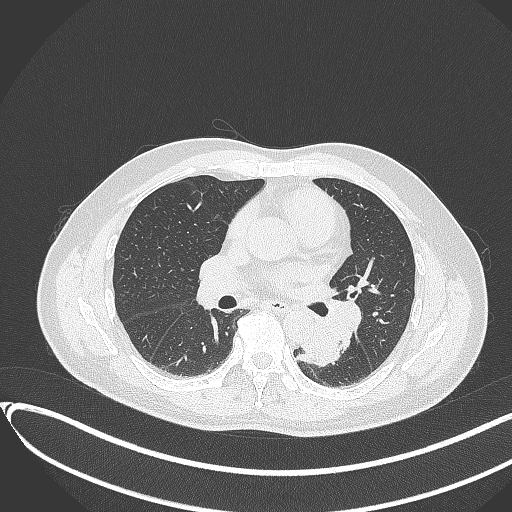
Chest CT, one axial slice. Position 183 of 417 along the scan axis. 120 kVp. Lung window (W 1500 / L -600 HU). 512 × 512 image matrix. Patient: male, 54 years. From the clinical record (not read from this slice): clinical TNM (as recorded): T3 N0 M0.
Annotated regions visible in this slice (rectangle marked by the reading radiologist):
- lung tumour (recorded histology: squamous cell carcinoma): box from (x=295, y=317) to (x=343, y=368) px